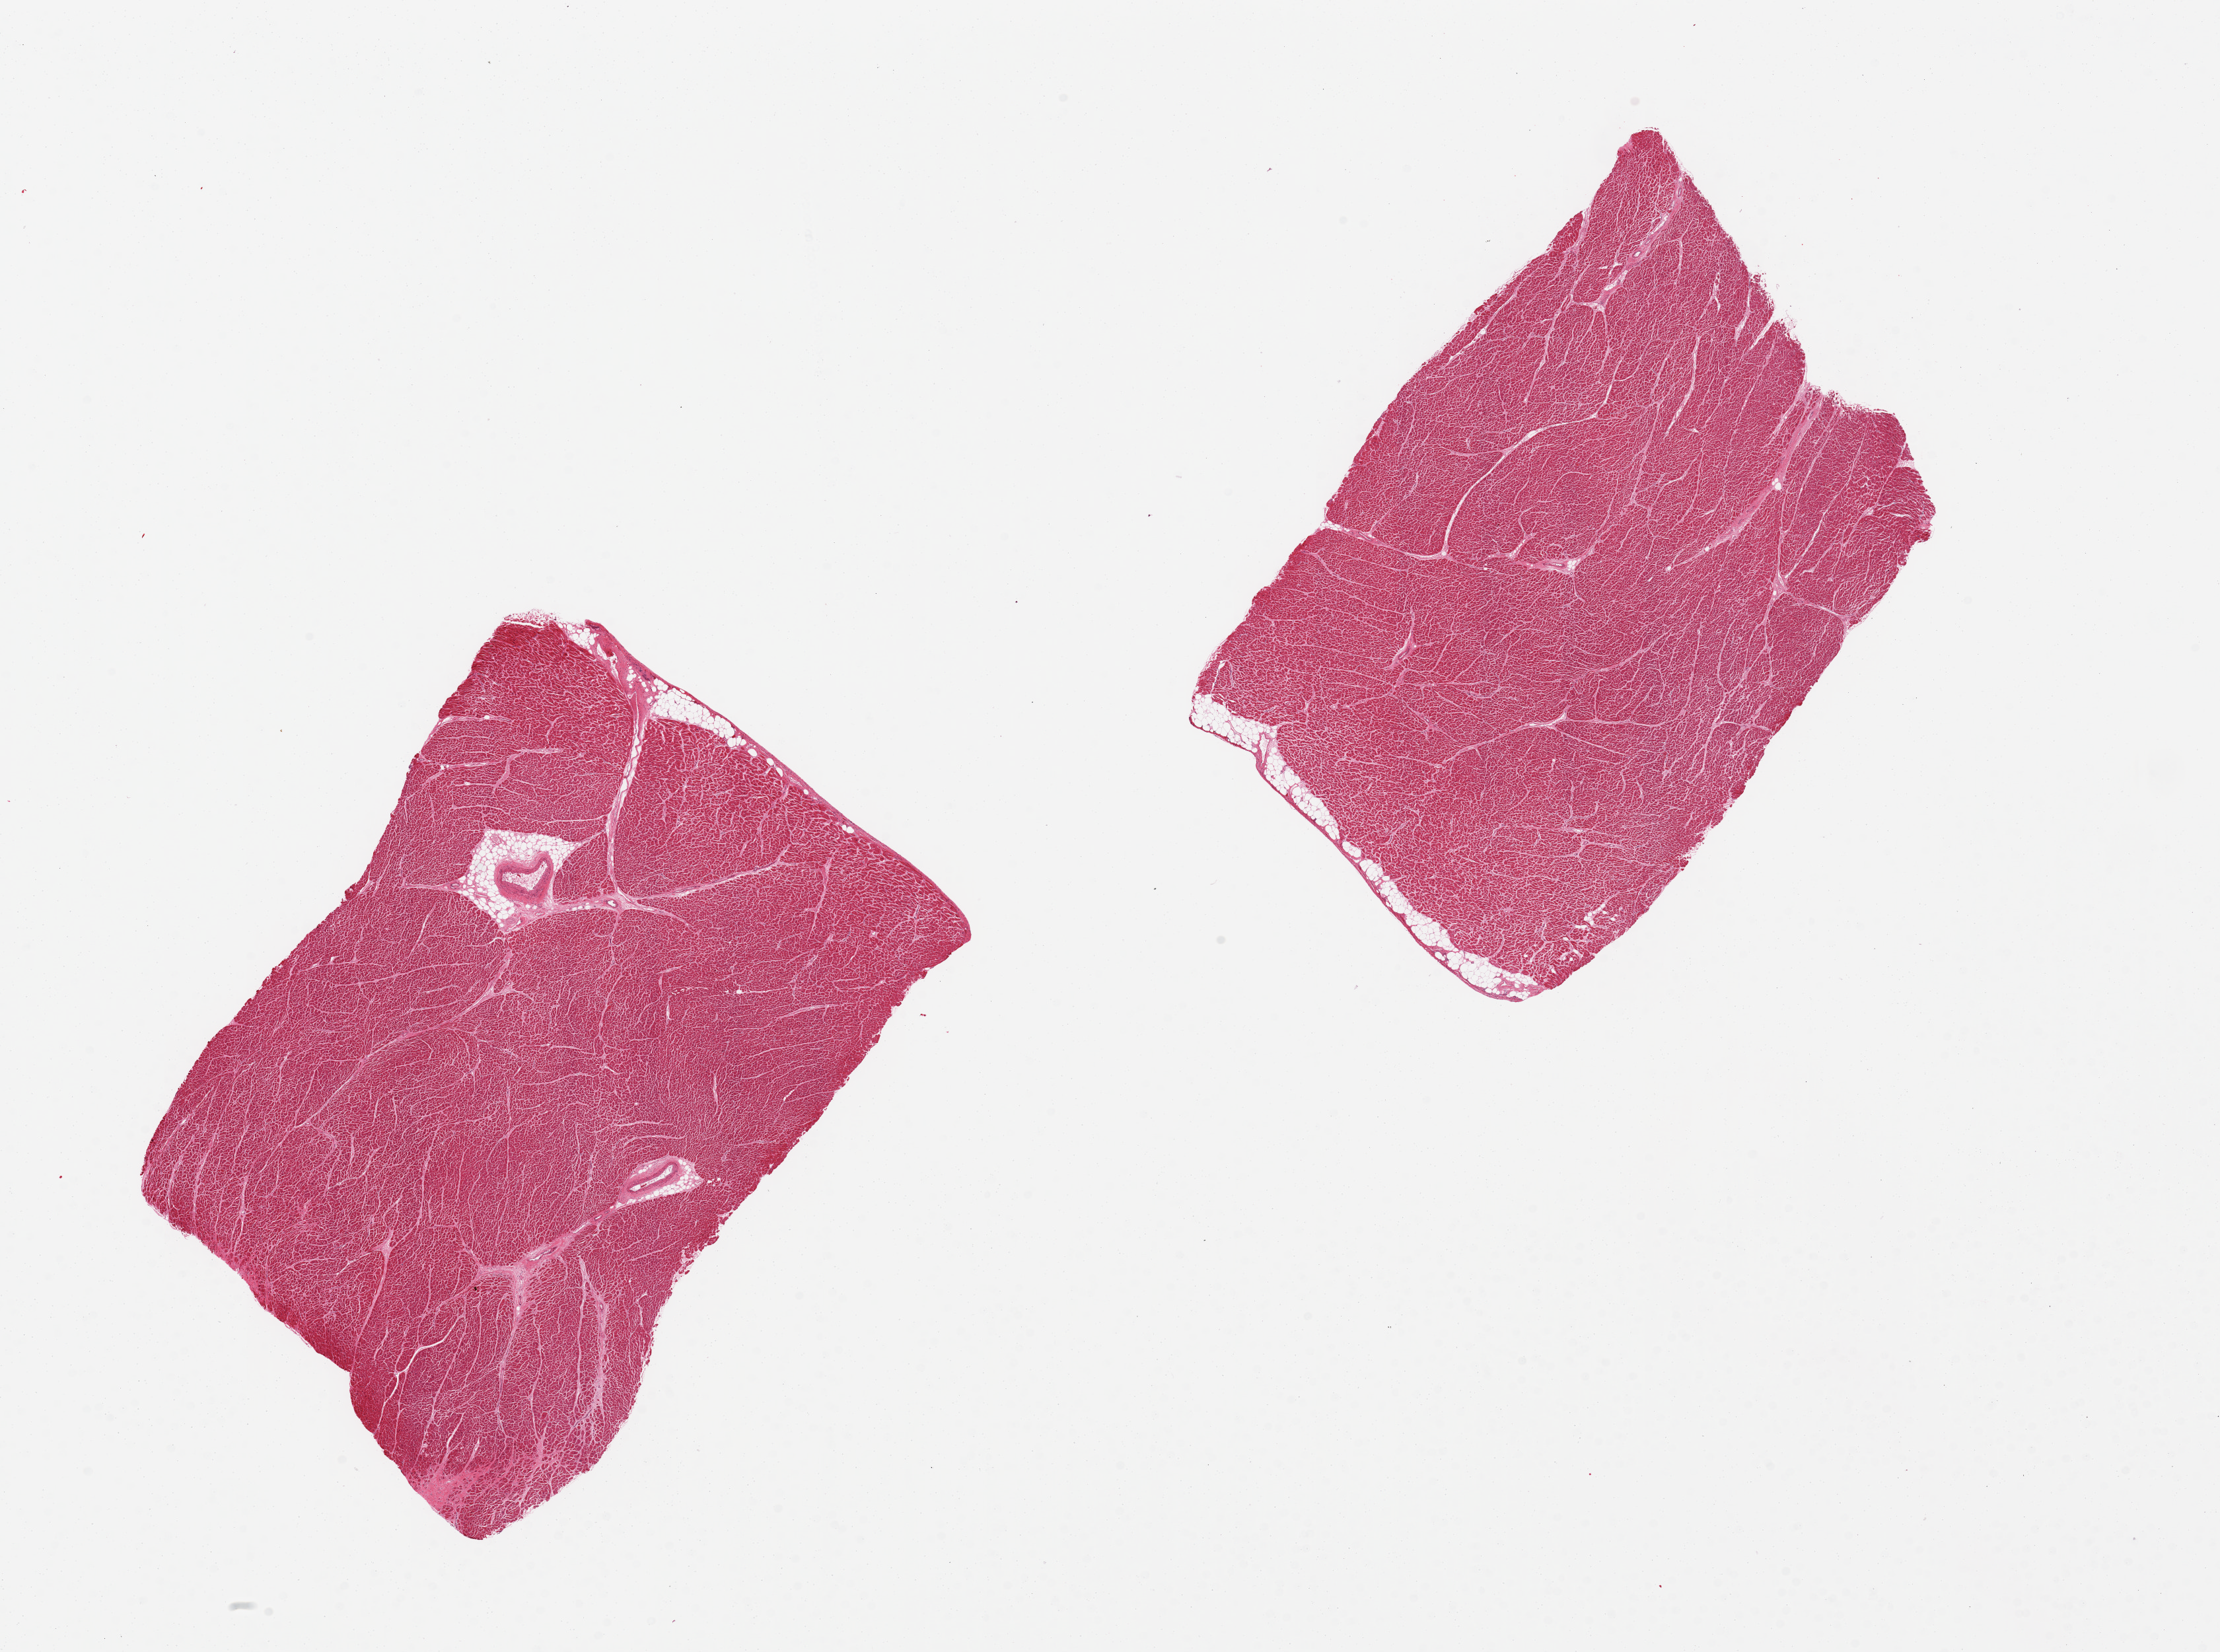
Haematoxylin and eosin whole-slide image, low-resolution overview of the scanned area, about 26.6 x 19.8 mm (acquisition: 20x scan). PAXgene-fixed paraffin-embedded (PFPE) section. Target tissue: heart. Donor tissue sample.
• pathologist's review note for this sample: 2 pieces